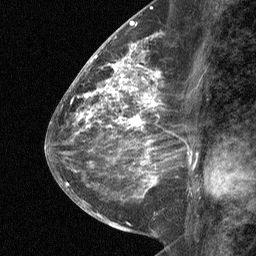
Breast MRI (dynamic contrast-enhanced), one sagittal slice; position 31 of 64 along the scan axis; dynamic contrast-enhanced study with each time point stored as its own series, time point 2 of 3 at this slice position (early post-contrast, ordered by acquisition time); 1.5 T; TE 4.8 ms, TR 27 ms; 2 mm slice thickness; 256 × 256 image matrix, field of view 180 × 180 mm. Patient: female, 59 years. From the clinical record (not read from this slice): setting: breast cancer imaged before/during neoadjuvant chemotherapy; receptor status: triple-negative.
Structures marked on this image (semi-automatically segmented with operator editing):
- analysis volume of interest (the breast-tissue region the enhancement analysis was run in; not a lesion): bounding box [x1, y1, x2, y2] px = [122, 58, 168, 109]
- tumour enhancement mask (voxels above the 90 % enhancement threshold inside the analysis volume of interest): [122, 58, 160, 107]